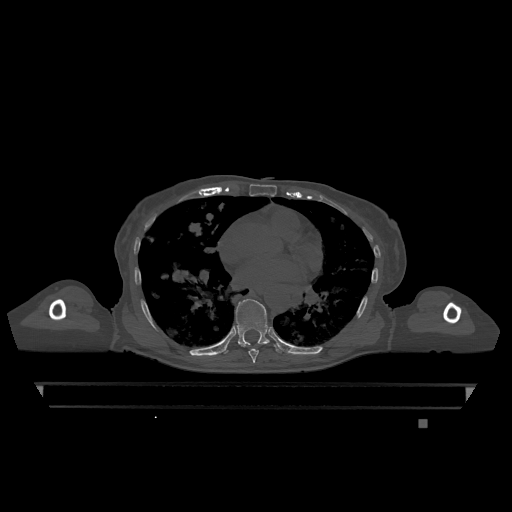
CT including the spine, one axial slice. Slice 710 of 1317 in the series (ordered by position). Bone window (W 1800 / L 400 HU). 0.5 mm slice thickness. 512 × 512 image matrix, field of view 500 × 500 mm. Patient: female, 74 years. Case-level facts recorded for this patient, not image findings: primary cancer: lung.
Outlined on this slice (semi-automatic segmentation, software-assisted and operator-edited):
- T7 vertebra: bounding box (x1, y1, x2, y2) in pixels: (248, 349, 259, 363)
- T9 vertebra: (224, 299, 282, 354)